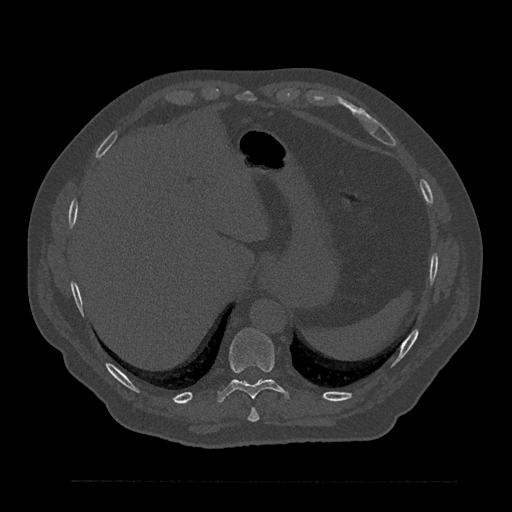
CT including the spine, one axial slice; position 348 of 797 along the scan axis; 120 kVp; bone window (W 1800 / L 400 HU); 0.5 mm slice thickness; 512 × 512 image matrix, field of view 430 × 430 mm. Male patient, age 61 years. Case-level facts recorded for this patient, not image findings: primary cancer: prostate.
Annotated regions visible in this slice (semi-automatically segmented with operator editing):
- T10 vertebra: bounding box <217,329,289,403> (left, top, right, bottom; pixels)
- T9 vertebra: <247,408,259,422>